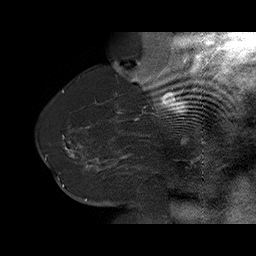
Breast MRI (dynamic contrast-enhanced), one sagittal slice. Position 50 of 75 along the scan axis. Dynamic contrast-enhanced series, time point 2 of 6 at this slice position (early post-contrast). 1.5 T. TE 4.5 ms, TR 32.4 ms. 256 × 256 image matrix, field of view 180 × 180 mm. Female patient. From the clinical record (not read from this slice): setting: breast cancer imaged before/during neoadjuvant chemotherapy; receptor status: HR-positive, HER2-negative.
Annotated regions visible in this slice (semi-automatically segmented with operator editing):
- analysis volume of interest (the breast-tissue region the enhancement analysis was run in; not a lesion): bounding box <58,134,166,191> (left, top, right, bottom; pixels)
- tumour enhancement mask (voxels above the 100 % enhancement threshold inside the analysis volume of interest): <62,141,128,186>